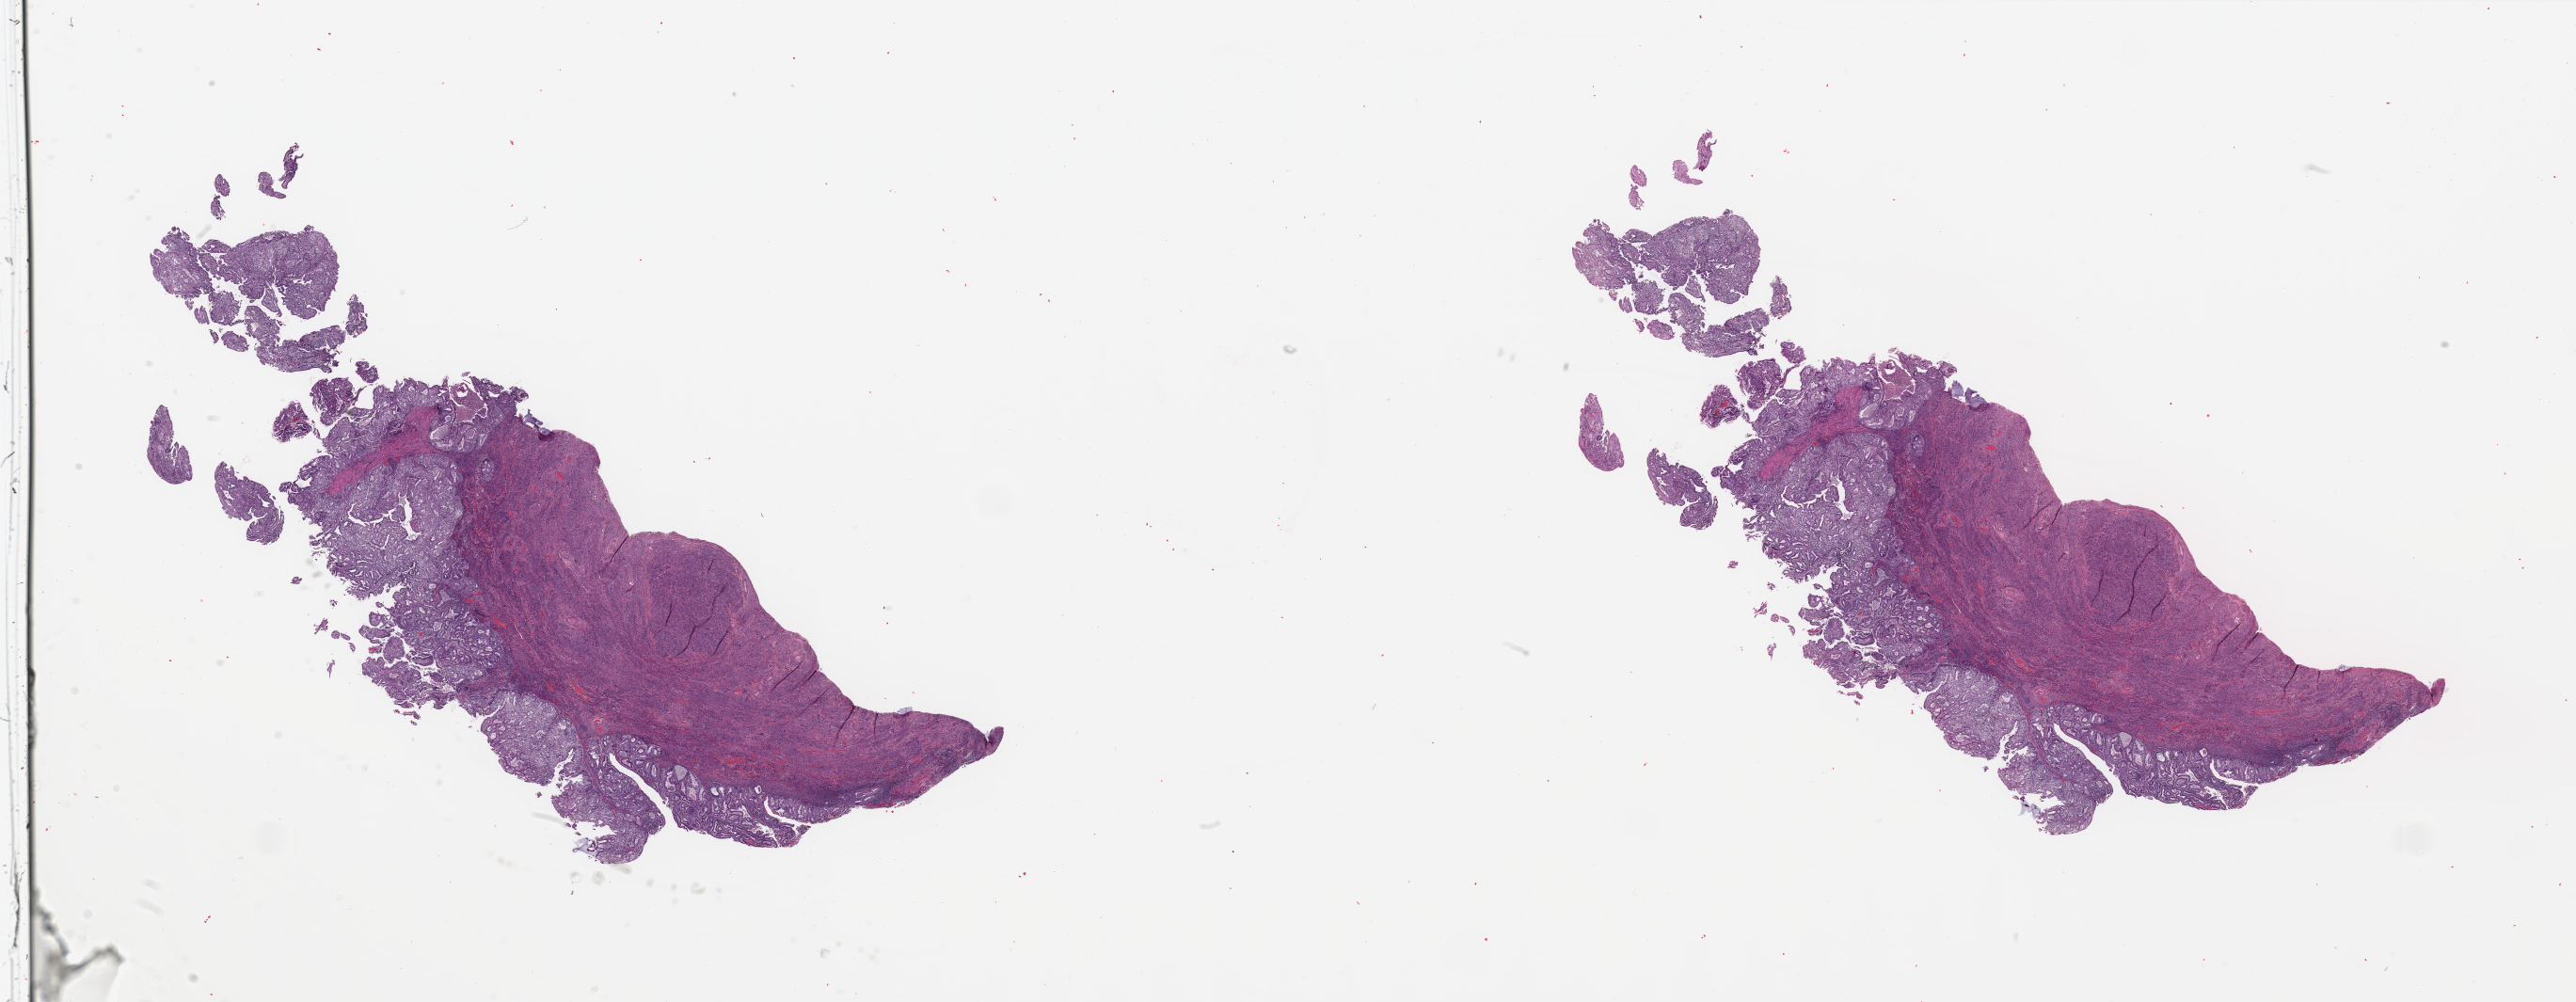
H&E-stained whole-slide image — a low-resolution overview of the entire scanned area, about 43.3 x 16.8 mm, uterus, tumour tissue. Female, 72 y/o. Histologic grade: G2 (moderately differentiated).
* histologic diagnosis: Endometrioid adenocarcinoma, NOS
* AJCC pathologic stage: I